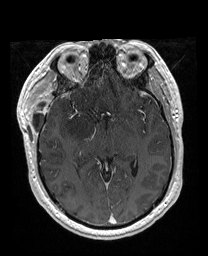
Brain MRI from a brain-tumour surgery series, one axial slice; position 104 of 176 along the scan axis; T1-weighted post-contrast; 1 mm slice thickness; 208 × 256 image matrix, field of view 208 × 256 mm. From the clinical record (not read from this slice): histopathology: Astrocytoma; WHO grade: 4; IDH mutation: yes.
Annotated regions visible in this slice (outlined manually by an expert reader):
- previous resection cavity: bounding box (x1, y1, x2, y2) in pixels: (75, 56, 91, 80)